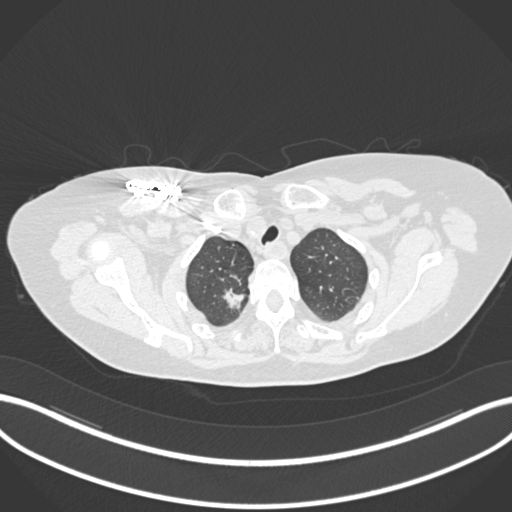
Chest CT, one axial slice; slice 156 of 176 in the series (ordered by position); reconstruction kernel B30f; 120 kVp; lung window (W 1500 / L -600 HU); 1 mm slice thickness; 512 × 512 image matrix. Female patient, age 72 years. Case-level facts recorded for this patient, not image findings: clinical TNM (as recorded): T1c N0 M0.
Annotated regions visible in this slice (bounding box drawn by a radiologist):
- lung tumour (recorded histology: adenocarcinoma): bounding box <222,286,247,316> (left, top, right, bottom; pixels)